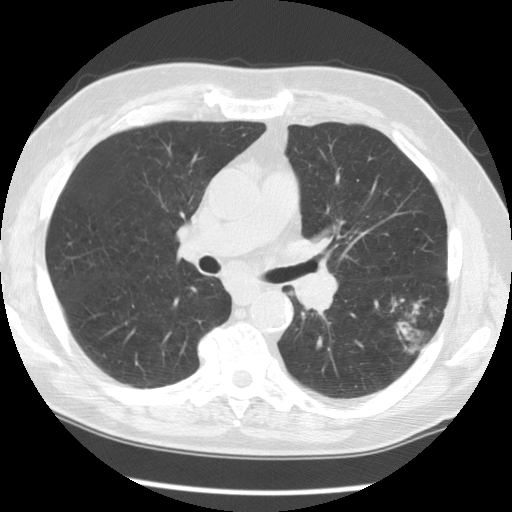
Low-dose screening chest CT, axial slice, baseline screening round, lung window (W 1500 / L -600 HU). Male, age 71 years at enrolment. Former smoker at enrolment.
Expert-annotated lung lesion, bounding box <373,287,456,365> (left, top, right, bottom; pixels). The screening reader recorded 3 non-calcified nodules or masses ≥4 mm on this exam (left lower lobe, right upper lobe, right upper lobe); which of them this box marks is not recorded. Official screen result: positive, change unspecified: nodule(s) >= 4 mm or enlarging nodule(s), mass(es), or other non-specific abnormalities suspicious for lung cancer. Participant outcome: lung cancer diagnosed 42 days after this screen — small cell carcinoma, NOS, left lower lobe, poorly differentiated (G3), stage IIIA (AJCC 6th edition), 19 mm at pathology.